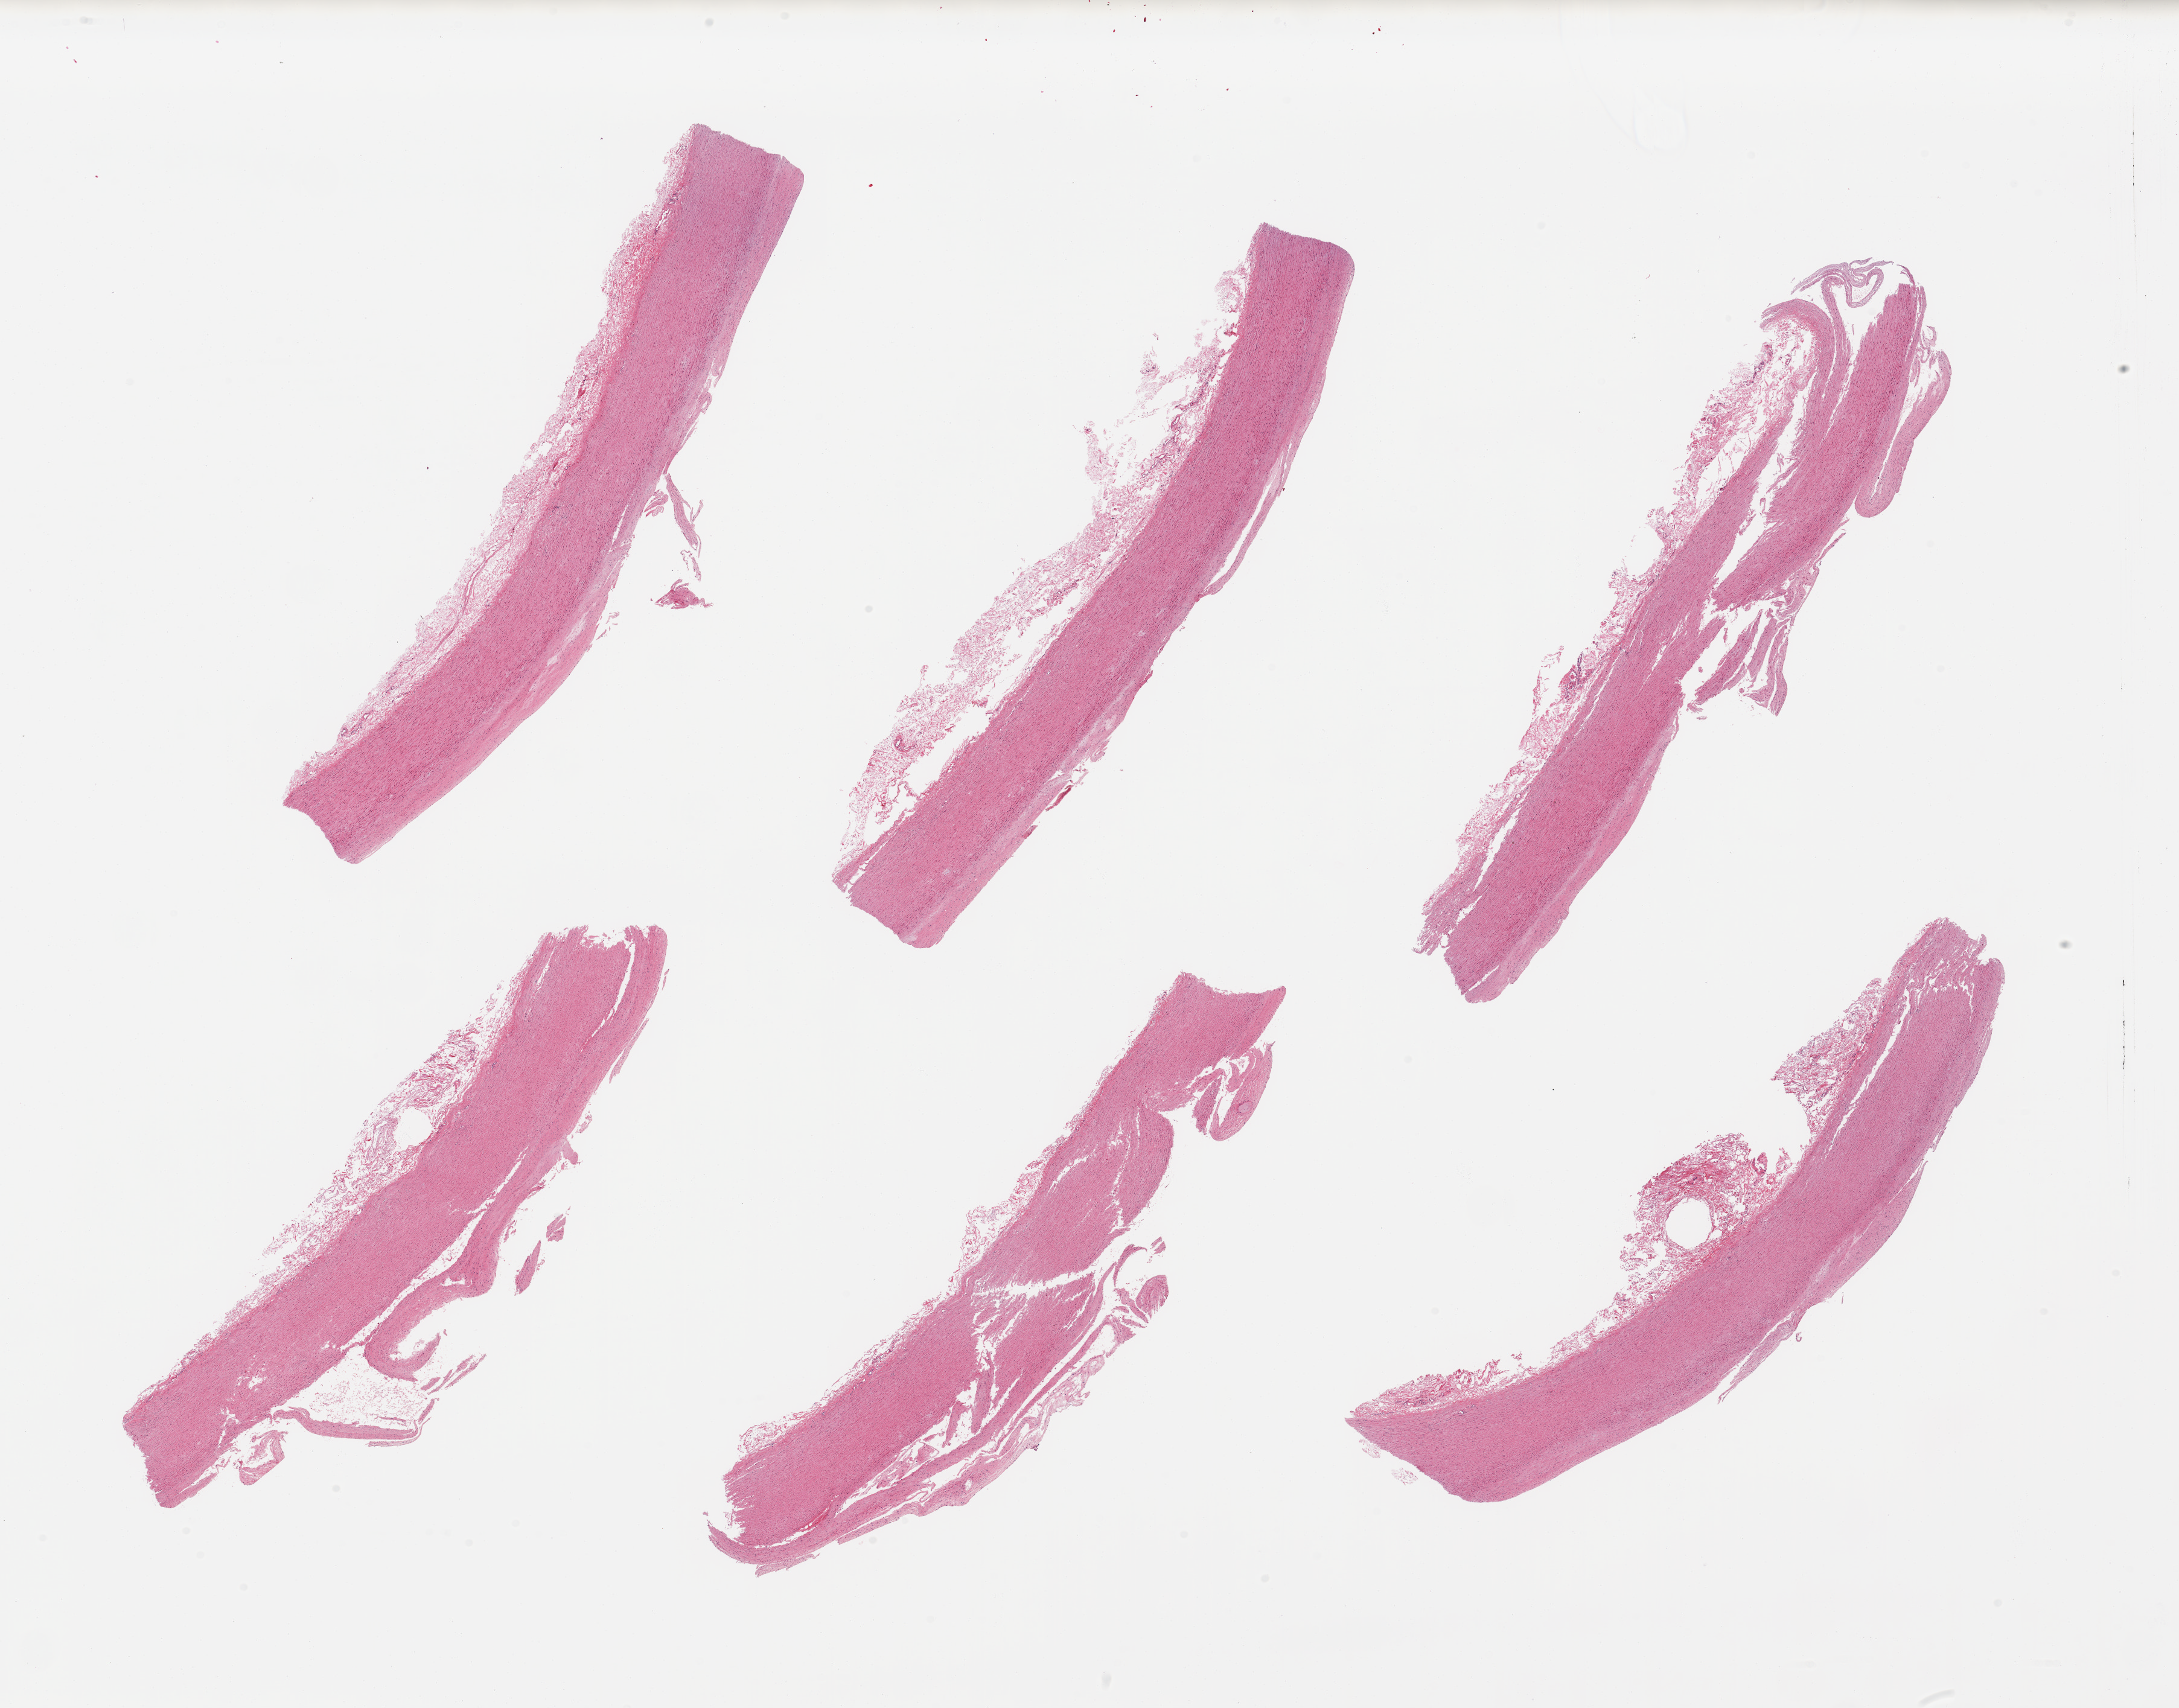
Hematoxylin and eosin (H&E) whole-slide image — whole scanned area (about 28.5 x 22.4 mm, from a 20x scan) shown as a low-resolution overview. PAXgene-fixed paraffin-embedded (PFPE) section. Section of aorta (target tissue). Donor tissue sample. Male donor.
* review note (as recorded): 6 pieces, atherosis up to ~0.5mm